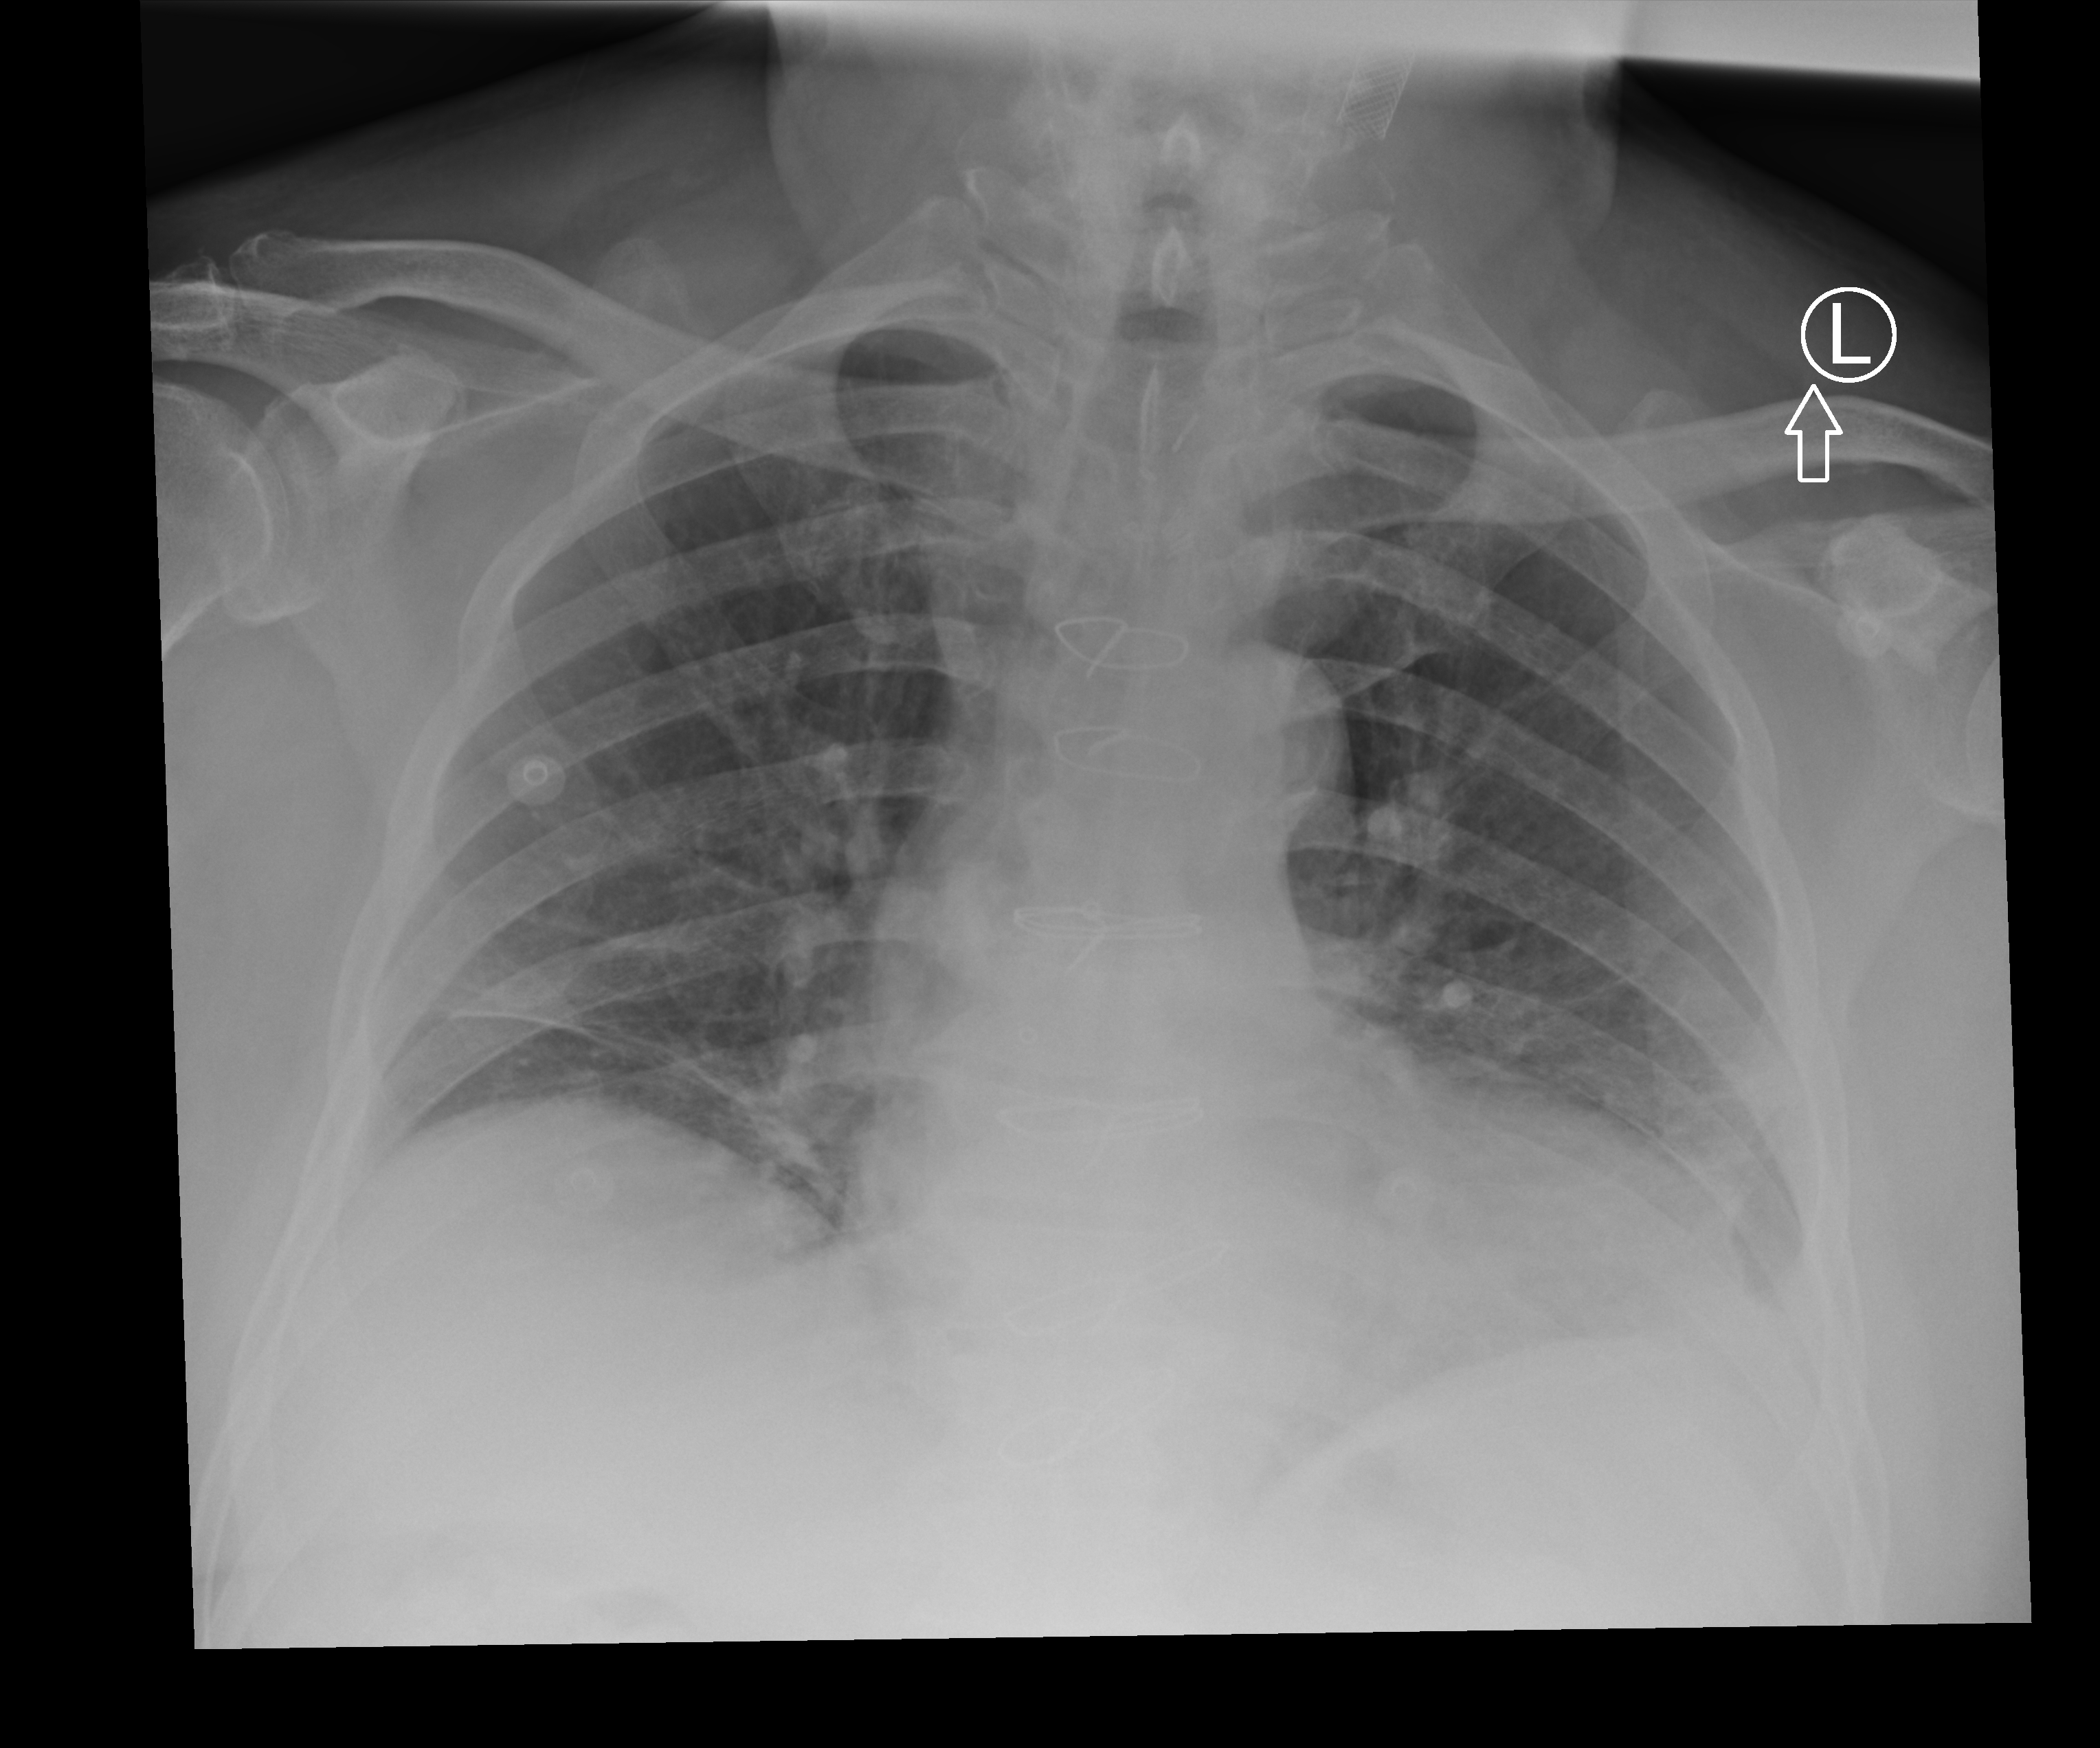
Chest radiograph; anteroposterior (AP) projection. Patient hospitalised with COVID-19; male, aged 75–90 years.
Hospital-stay facts (about this admission, not read from this image; timing relative to this image not recorded): admitted to intensive care during this hospital stay: no.